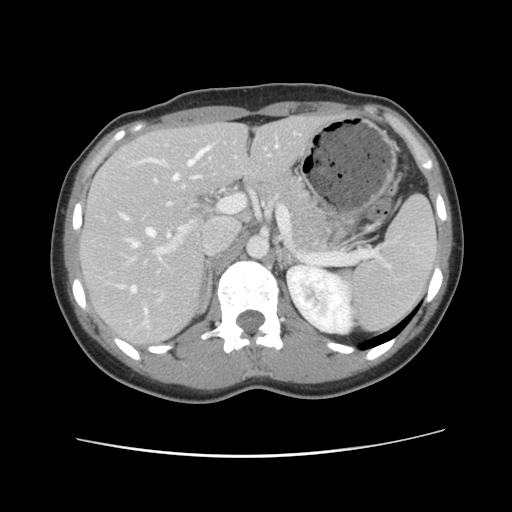
Contrast-enhanced abdominal CT, one axial slice; position 65 of 134 along the scan axis; intravenous contrast given; soft-tissue window (W 400 / L 40 HU); 512 × 512 image matrix, field of view 339 × 339 mm. Female patient, age 33 years. Case-level facts recorded for this patient, not image findings: diagnosis: colorectal cancer liver metastases, imaged before liver resection; multiple liver metastases: yes; largest metastasis: 4.5 cm; disease in both lobes: yes.
Annotated regions visible in this slice (outlined manually by an expert reader):
- hepatic veins: box from (x=121, y=145) to (x=278, y=316) px
- liver: (x=81, y=115)–(x=325, y=347)
- planned liver remnant (the part of the liver to remain after resection): (x=80, y=115)–(x=326, y=346)
- portal vein (with intrahepatic branches): (x=111, y=195)–(x=235, y=303)